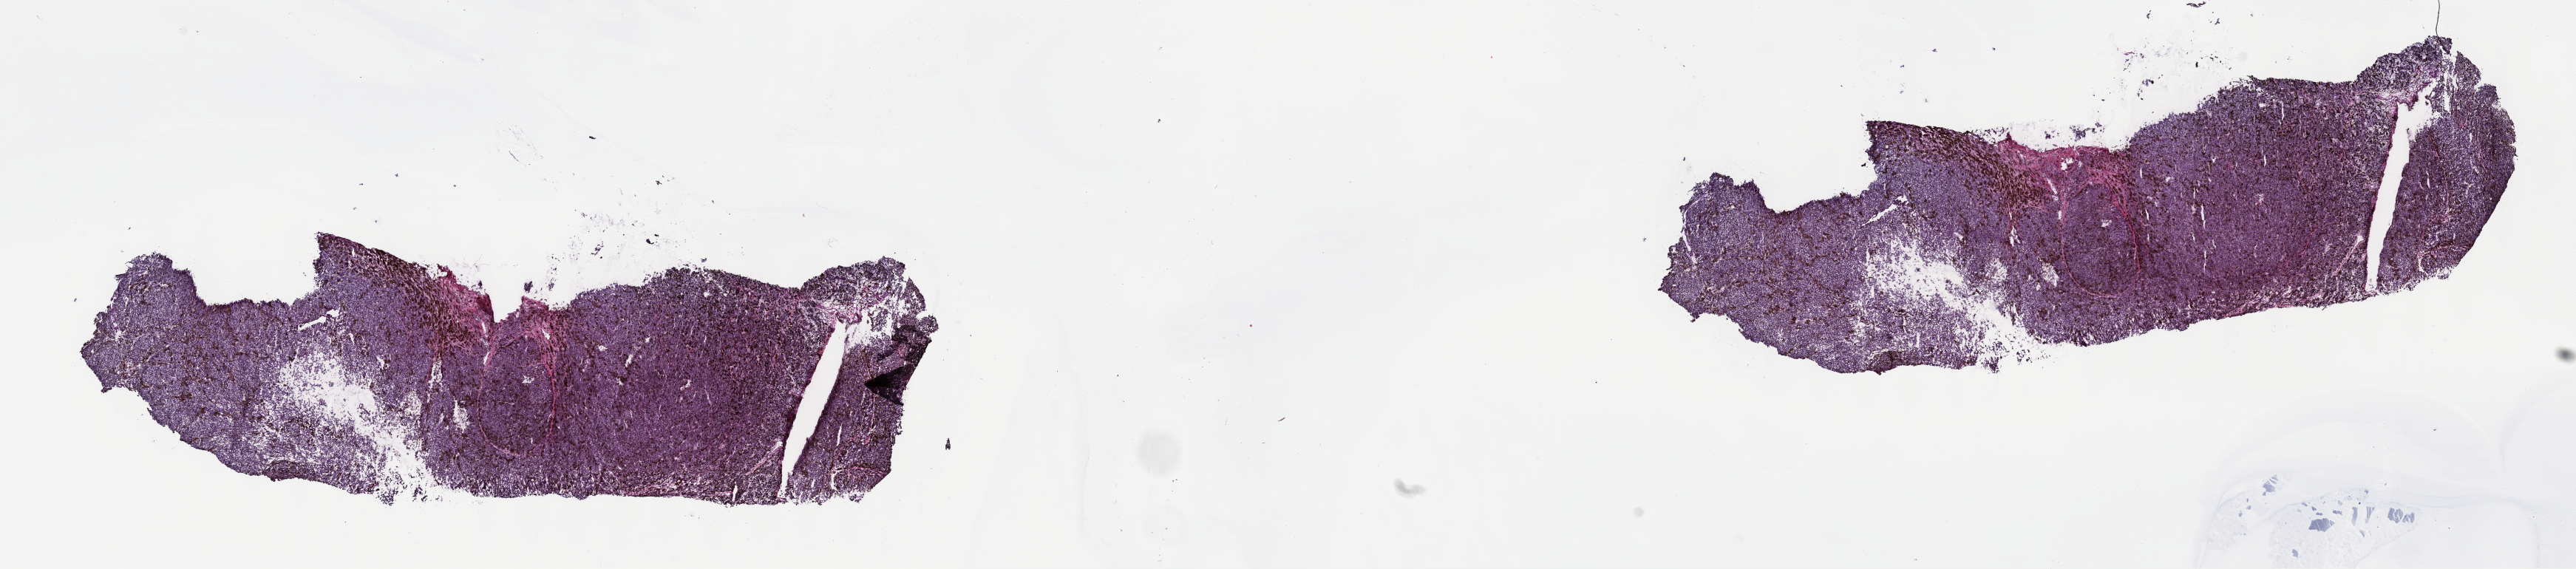
Digitized H&E tissue section (whole slide) — shown as a low-resolution overview of the whole scanned area (about 28.2 x 6.2 mm); frozen section; sample: primary tumour, uvea. Female patient; age at initial diagnosis 46 years. Composition of this section per pathologist review: tumour cells 100%, tumour nuclei 80%, normal cells 0%, stromal cells 0%, necrosis 0%. Infiltration values recorded for this section: lymphocyte infiltration 1%, monocyte infiltration 0%, neutrophil infiltration 0%.
* histologic diagnosis: Epithelioid cell melanoma (choroid)
* AJCC pathologic stage: IIB (7th edition)